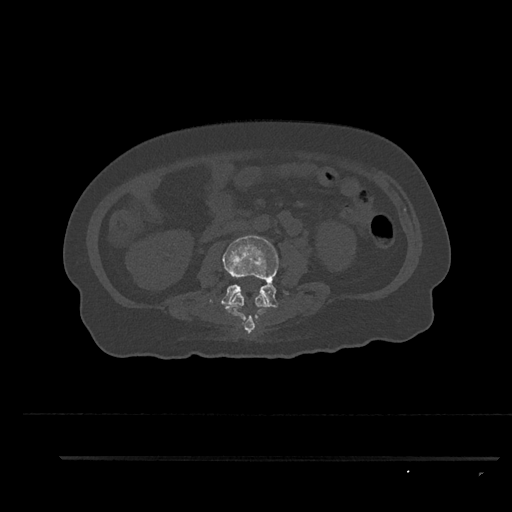
CT including the spine, one axial slice; position 112 of 797 along the scan axis; reconstruction kernel Br40s/3; 120 kVp; bone window (W 1800 / L 400 HU); 0.5 mm slice thickness; 512 × 512 image matrix, field of view 408 × 408 mm. Female patient, age 44 years. Case-level facts recorded for this patient, not image findings: primary cancer: renal; vertebrae with lytic lesions (as recorded): L1.
Outlined on this slice (semi-automatically segmented with operator editing):
- L2 vertebra: bounding box (x1, y1, x2, y2) in pixels: (225, 293, 267, 334)
- L3 vertebra: (220, 235, 289, 309)